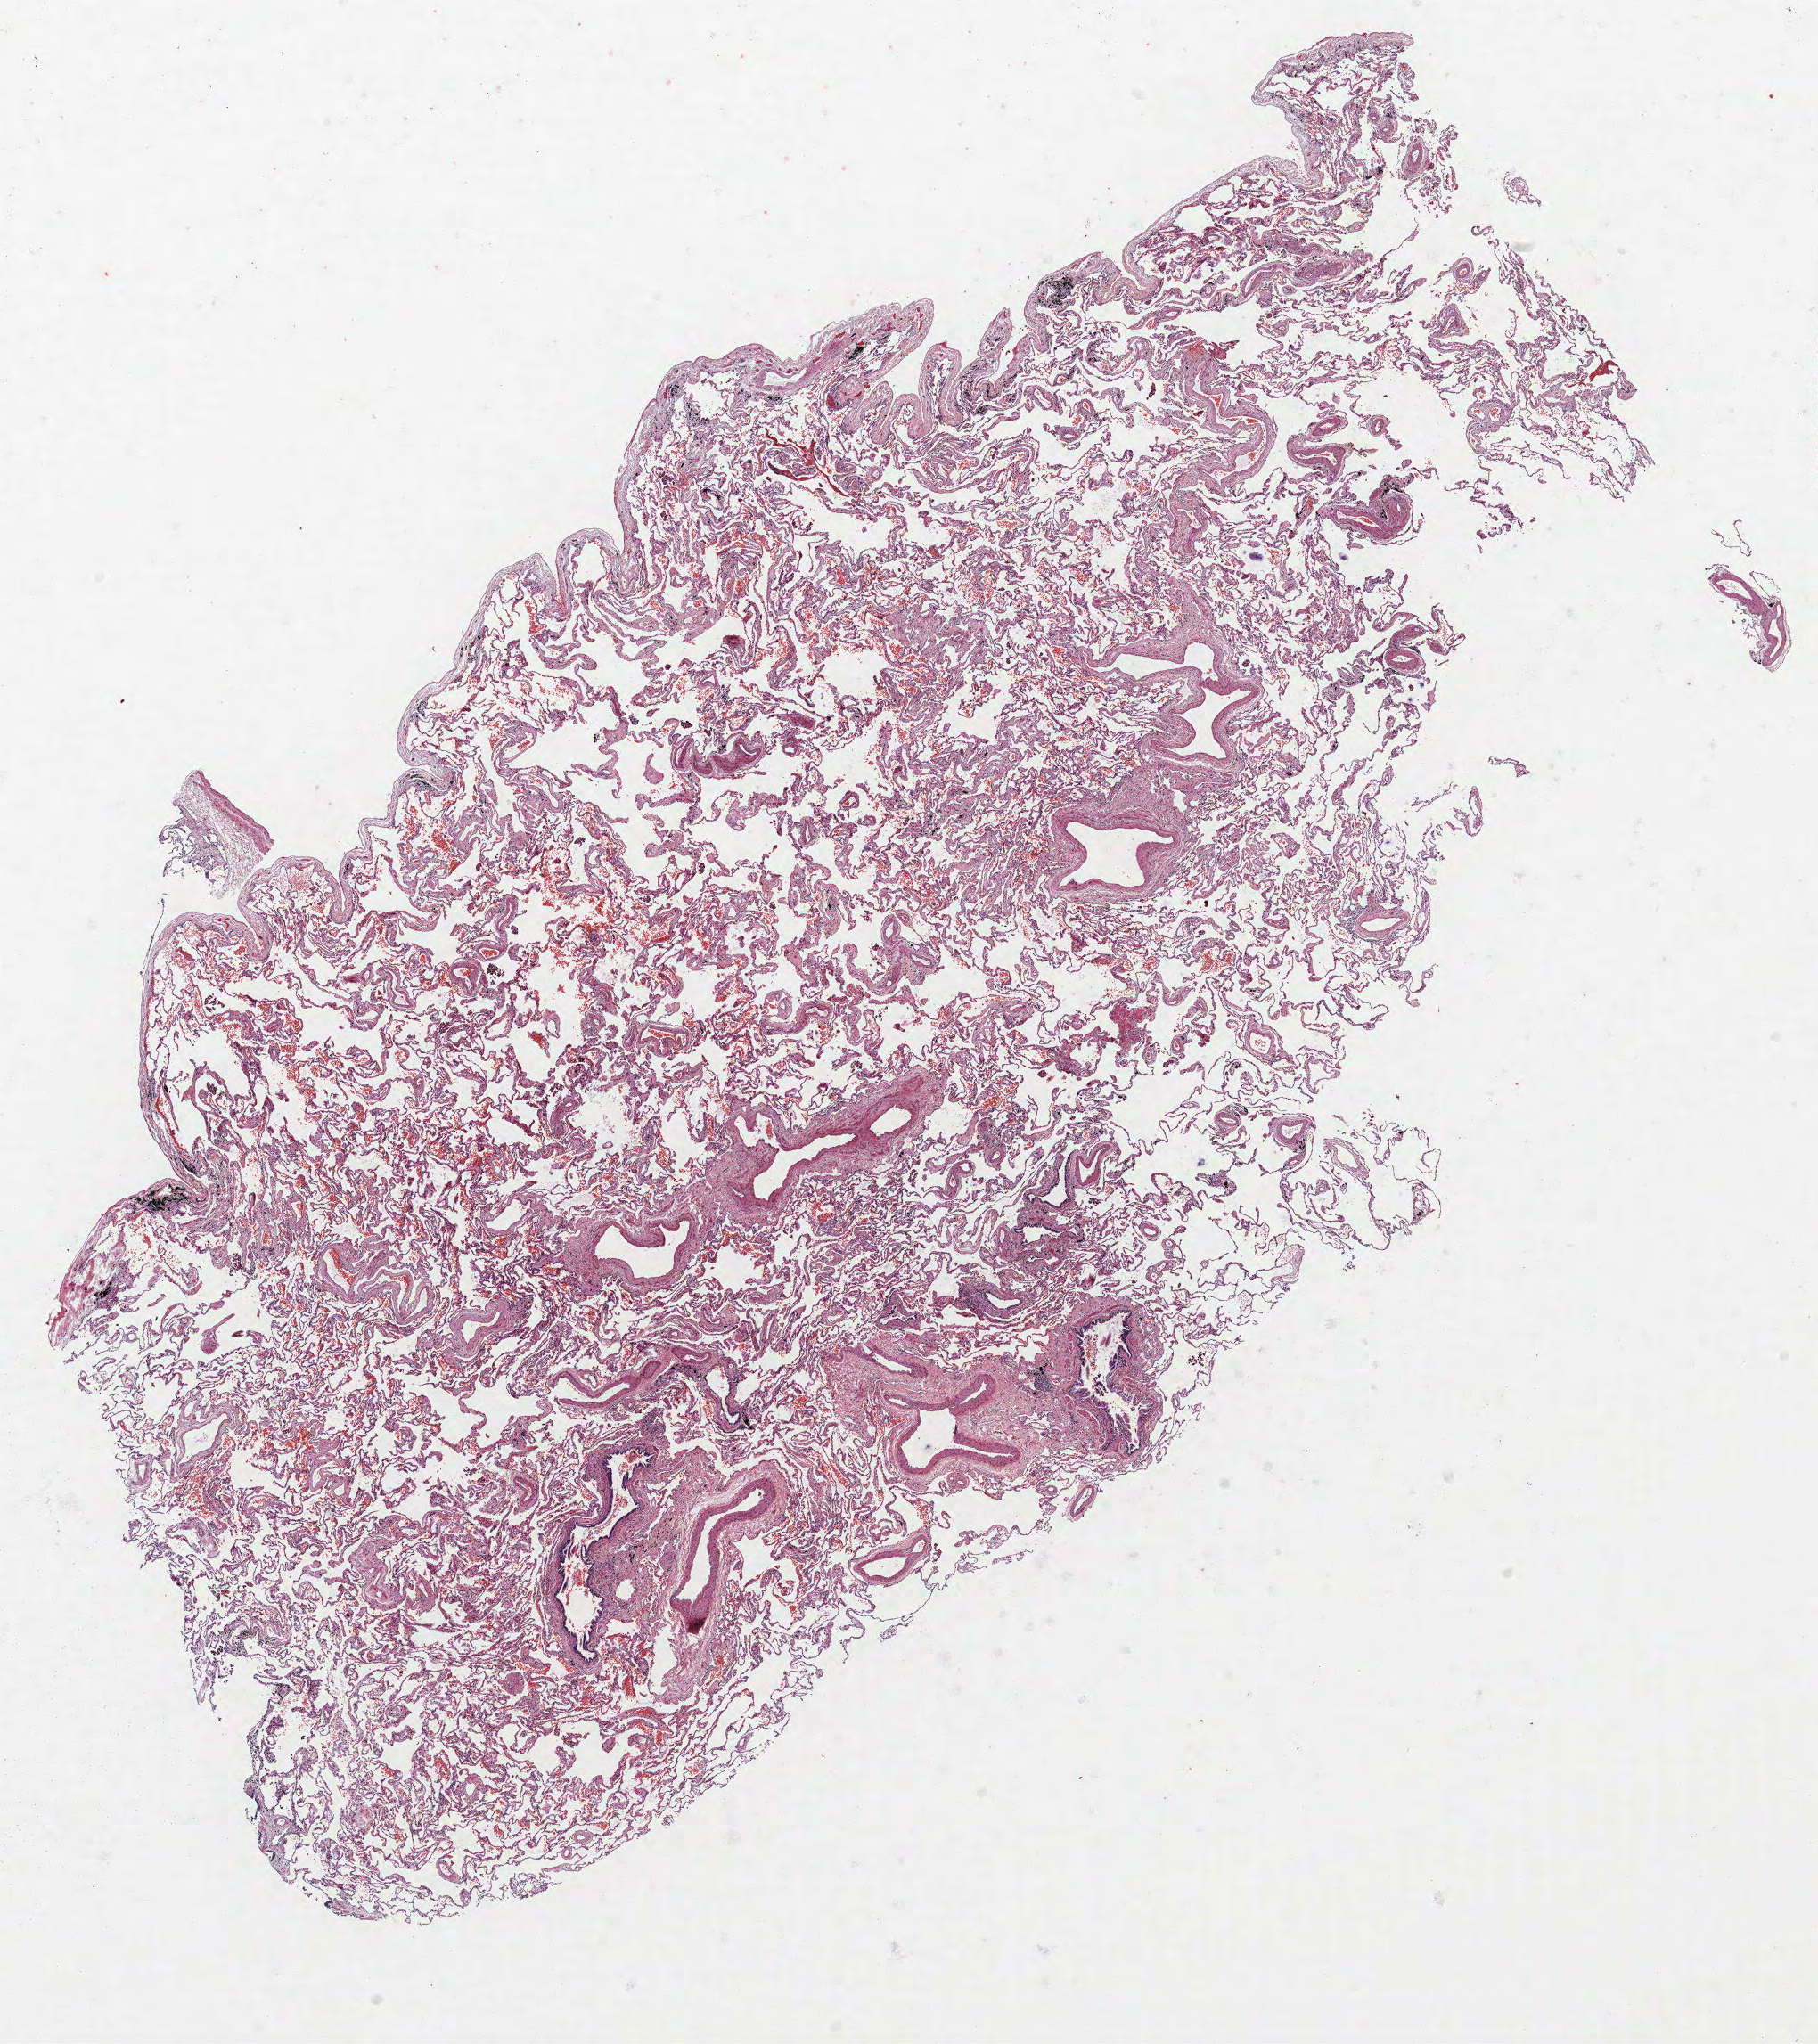
Whole-slide histology image, Hematoxylin and eosin (H&E) stained, a low-resolution overview of the entire scanned area, about 16.3 x 18.4 mm, formalin-fixed paraffin-embedded (FFPE) section, lung tissue. Female, age 65 at enrolment. Former smoker at enrolment. Grade: moderately differentiated (G2).
* tumour size (pathology): 25 mm
* primary tumour location (clinical record): right lower lobe
* stage (AJCC 6th edition): IA
* participant's lung-cancer diagnosis: Adenocarcinoma, NOS